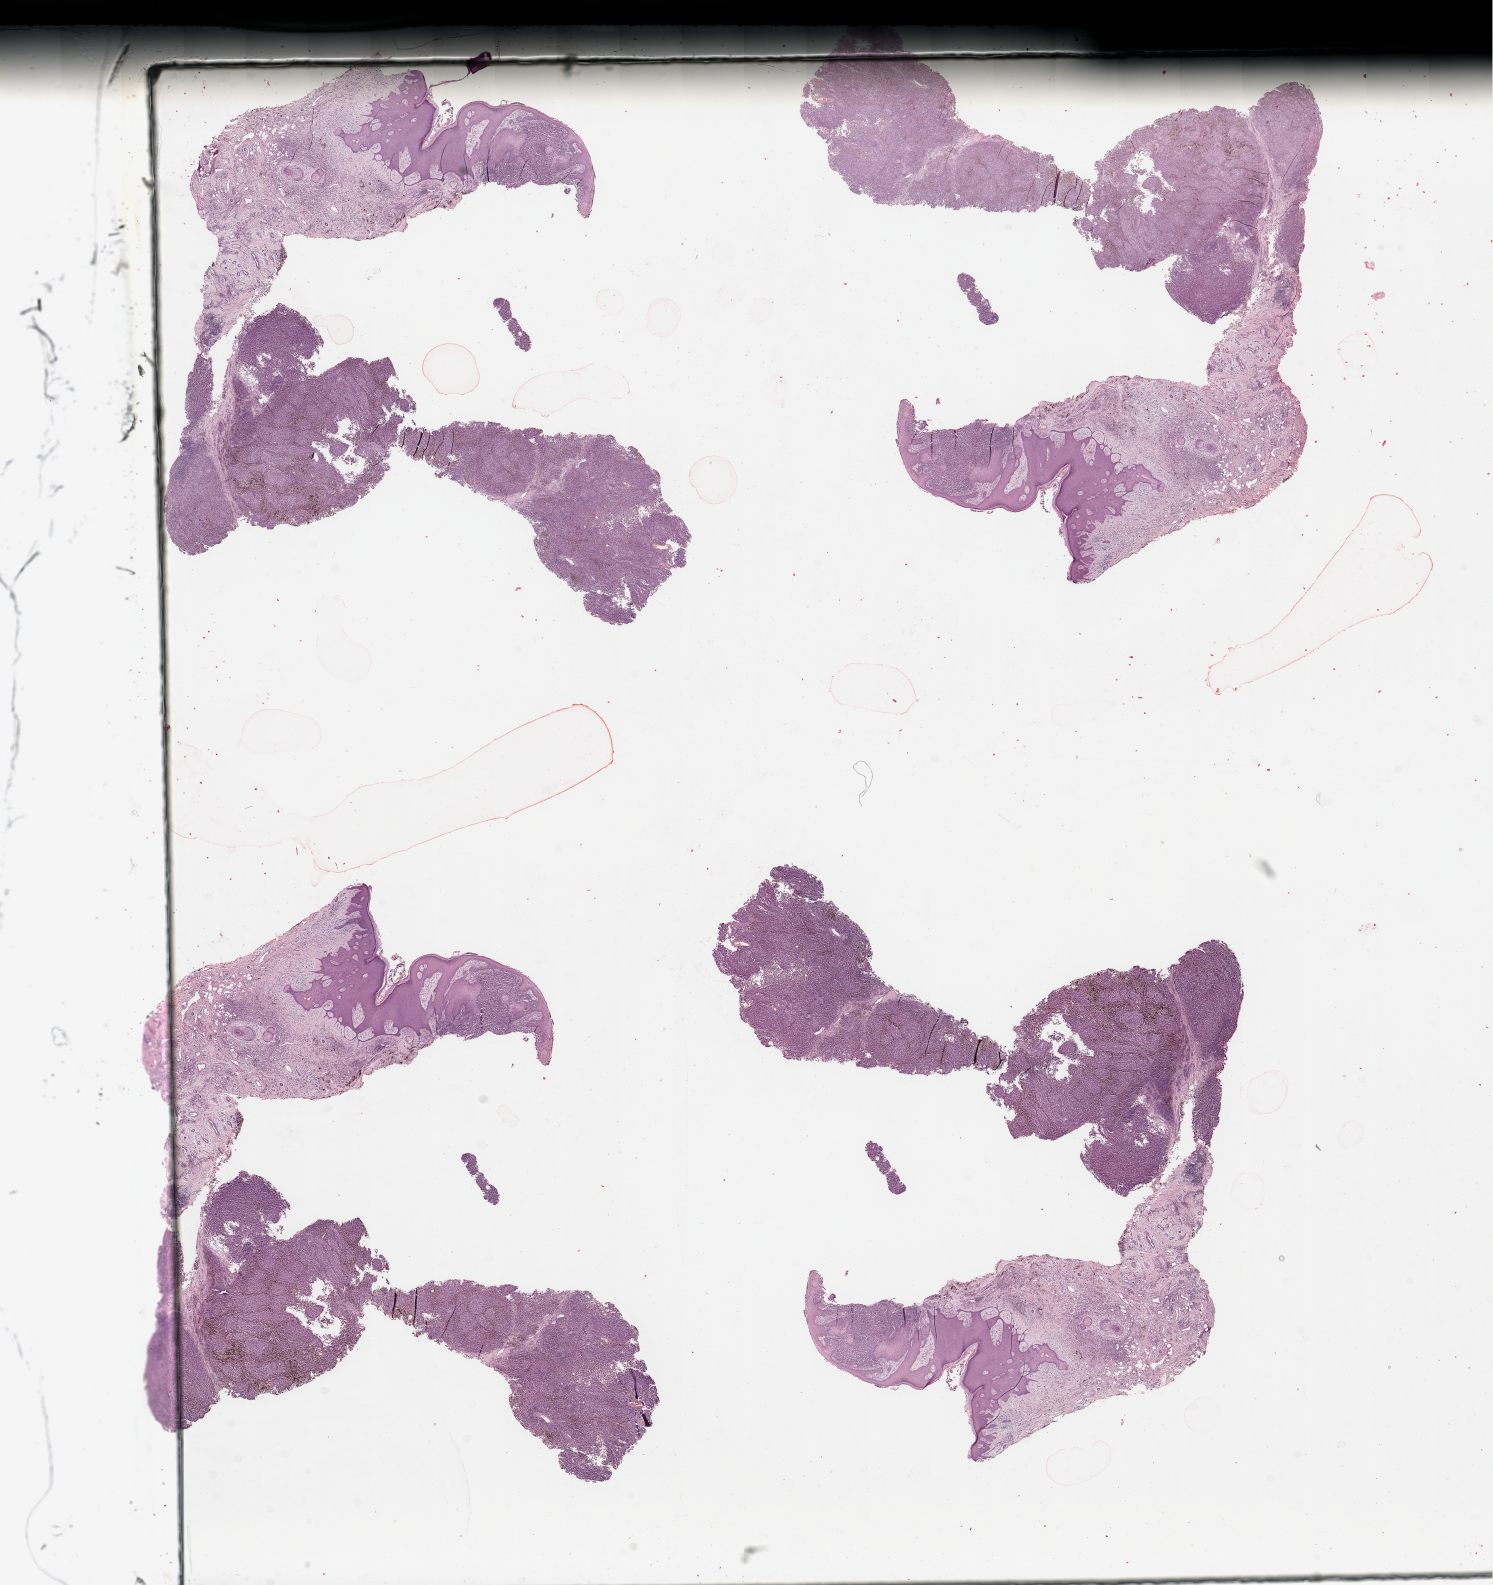
Digitized H&E tissue section (whole slide), shown as a low-resolution overview of the whole scanned area (about 23.6 x 25.1 mm). Melanoma tumour tissue; sampled site not recorded. Male, 60 y/o.
Diagnosis: Malignant melanoma, NOS. Primary tumour site (as recorded): trunk.